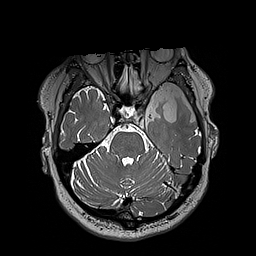
Brain MRI from a brain-tumour surgery series, one axial slice; slice 140 of 192 in the series (ordered by position); 1 mm slice thickness; 256 × 256 image matrix, field of view 250 × 250 mm. Case-level facts recorded for this patient, not image findings: histopathology: Oligodendroglioma; WHO grade: 3; IDH mutation: yes; tumour location: Left Sylvian Fissure (Temporal).
Annotated regions visible in this slice (expert manual segmentation):
- tumour: box from (x=128, y=69) to (x=195, y=121) px